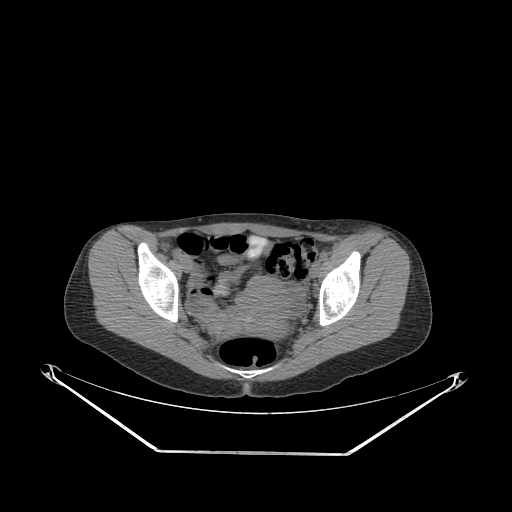
CT of an extremity soft-tissue mass (from a PET/CT study), one axial slice. Position 80 of 267 along the scan axis. Reconstruction kernel SOFT. 140 kVp. Soft-tissue window (W 400 / L 40 HU). 512 × 512 image matrix, field of view 500 × 500 mm. Female patient. Case-level facts recorded for this patient, not image findings: histological type: leiomyosarcoma; grade: high; site of the primary tumour: groin.
Outlined on this slice (expert contour drawn on MRI and transferred to this co-registered scan by the dataset authors):
- gross tumour volume including surrounding oedema: box from (x=322, y=237) to (x=389, y=257) px